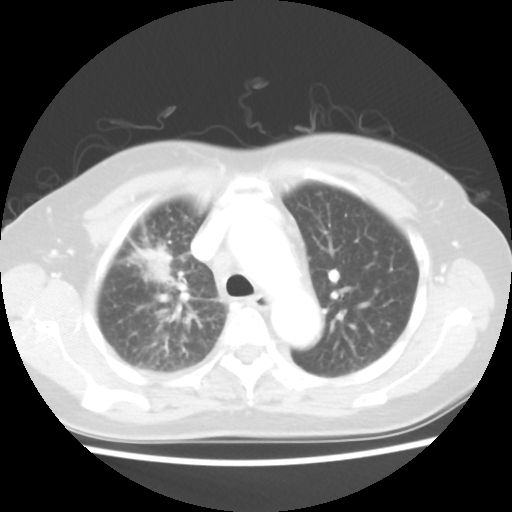
Chest CT, one axial slice. Slice 33 of 48 in the series (ordered by position). 100 kVp. Lung window (W 1500 / L -600 HU). 512 × 512 image matrix. Patient: female, 55 years. From the clinical record (not read from this slice): clinical TNM (as recorded): T1b N3 M1a.
Structures marked on this image (bounding box drawn by a radiologist):
- lung tumour (recorded histology: adenocarcinoma): bounding box <135,247,173,282> (left, top, right, bottom; pixels)